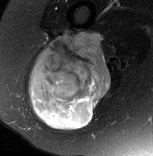
MRI of an extremity soft-tissue mass, one axial slice; slice 41 of 77 in the series (ordered by position); T2-weighted fat-saturated; MR volume resampled by the dataset authors to the PET/CT grid (not the native acquisition matrix); 3.27 mm slice thickness; 153 × 156 image matrix. Female patient. From the clinical record (not read from this slice): histological type: synovial sarcoma; grade: intermediate; site of the primary tumour: right buttock.
Annotated regions visible in this slice (expert contour drawn on MRI and transferred to this co-registered scan by the dataset authors):
- gross tumour volume including surrounding oedema: bounding box <28,31,111,130> (left, top, right, bottom; pixels)
- gross tumour volume (mass): <28,31,111,130>